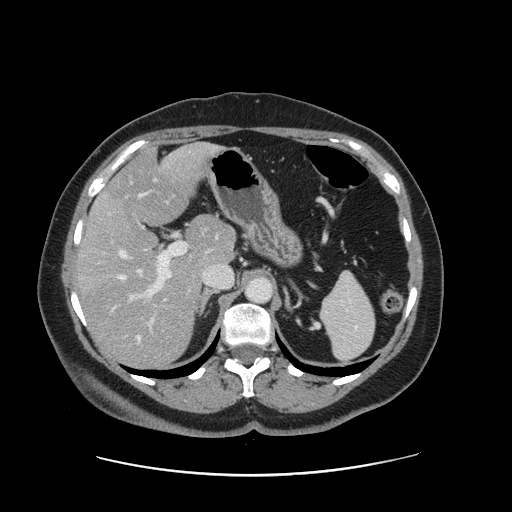
Contrast-enhanced abdominal CT, one axial slice. 120 kVp. Intravenous contrast given. Soft-tissue window (W 400 / L 40 HU). 2.5 mm slice thickness. 512 × 512 image matrix, field of view 398 × 398 mm. Female patient, age 62 years. Case-level facts recorded for this patient, not image findings: diagnosis: colorectal cancer liver metastases, imaged before liver resection; multiple liver metastases: no; largest metastasis: 2.5 cm; chemotherapy before resection: yes.
Annotated regions visible in this slice (manually delineated by an expert):
- hepatic veins: bounding box (x1, y1, x2, y2) in pixels: (113, 193, 148, 341)
- liver: (80, 145, 234, 366)
- planned liver remnant (the part of the liver to remain after resection): (106, 144, 234, 267)
- portal vein (with intrahepatic branches): (123, 242, 187, 339)